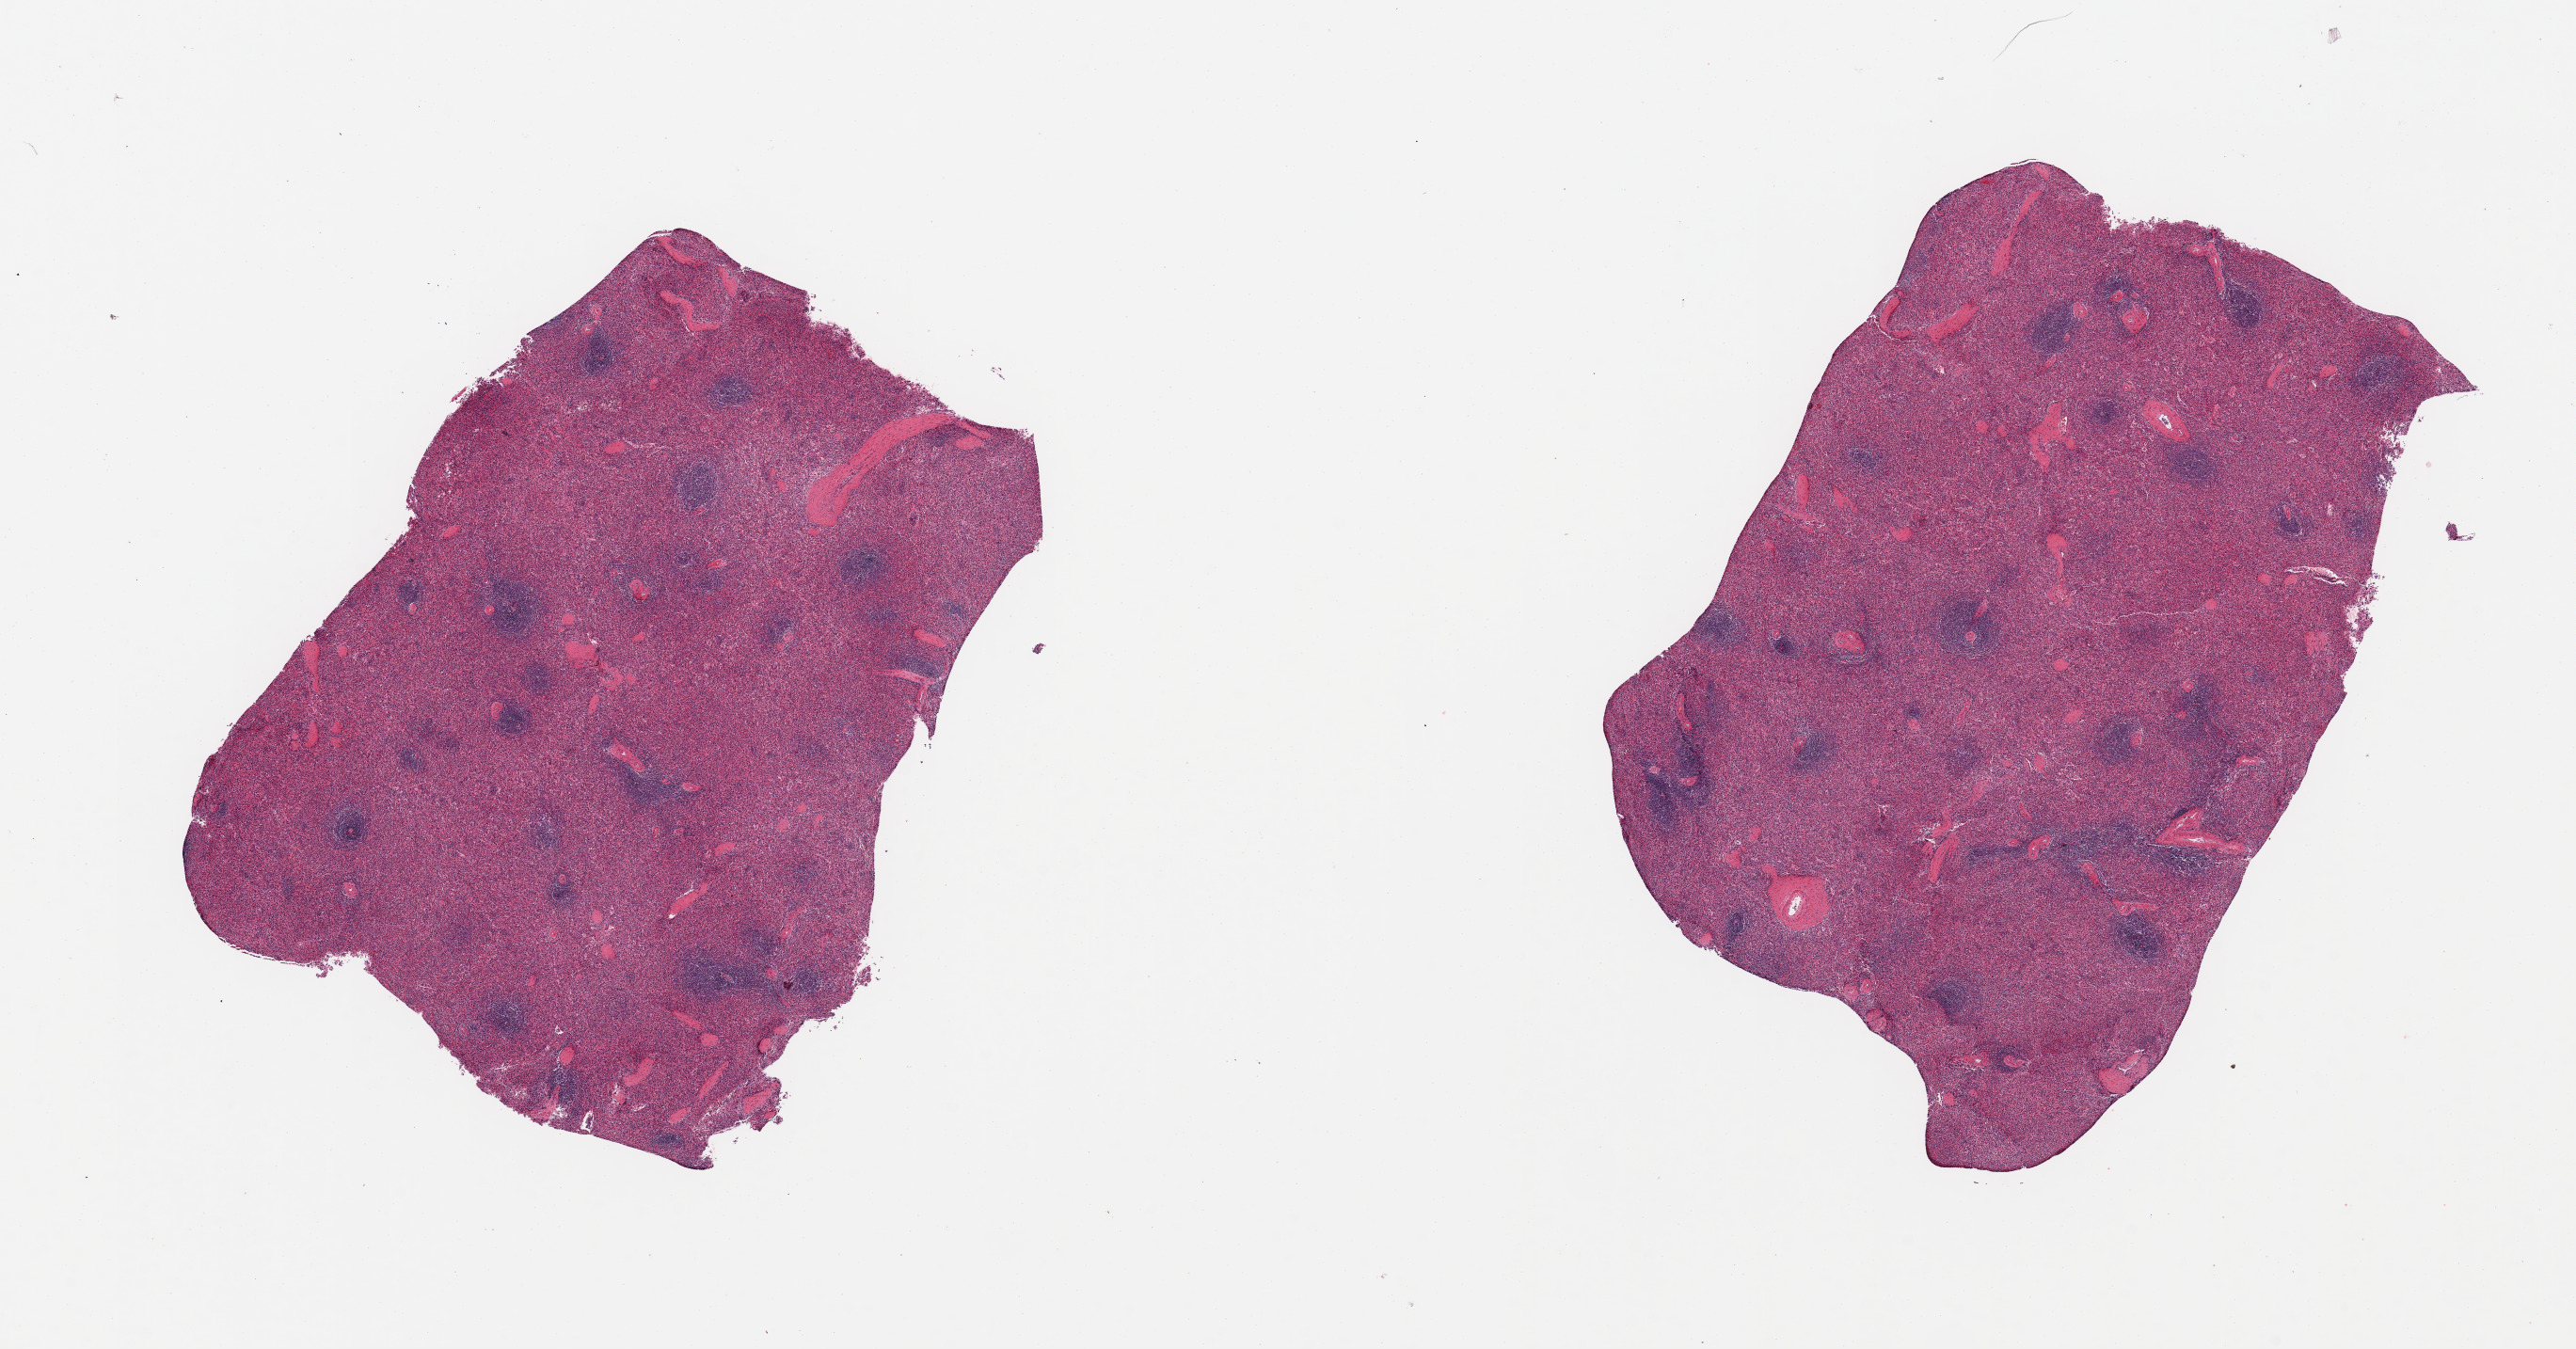
Digitized hematoxylin and eosin (H&E)-stained section — low-resolution overview of the scanned area, about 21.7 x 11.3 mm, PAXgene-fixed, paraffin-embedded tissue, target tissue: spleen, donor tissue sample. Donor sex: male.
Pathologist's review note for this sample: 2 pieces.